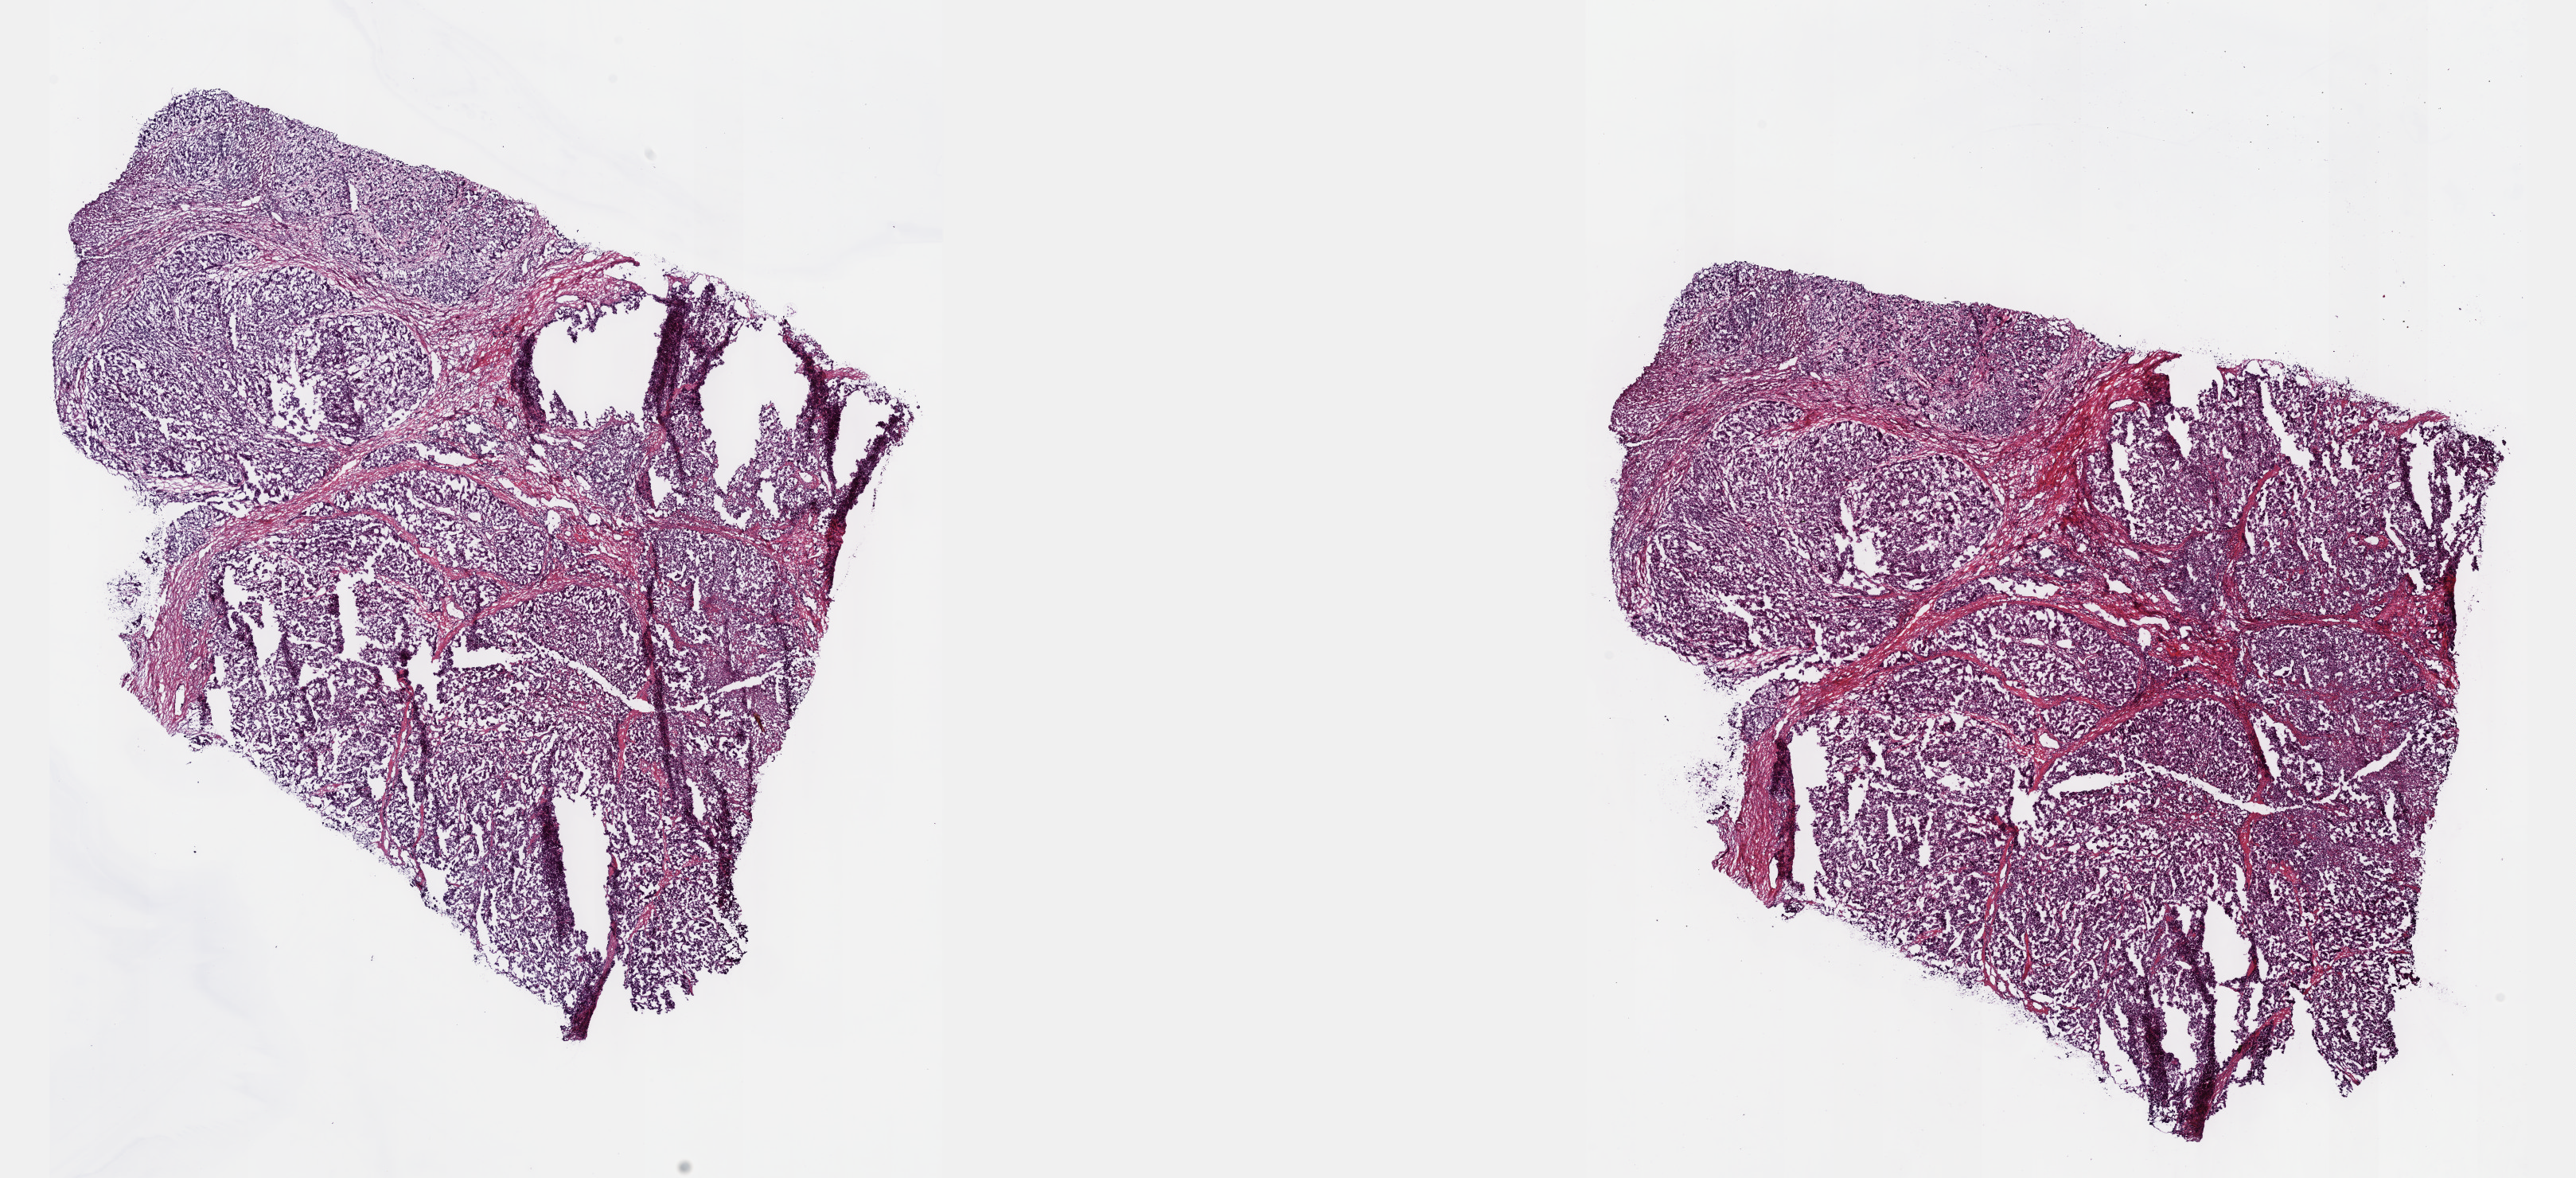
Digitized Hematoxylin and eosin (H&E) stained tissue section (whole slide), a low-resolution overview of the entire scanned area, about 26.2 x 12.0 mm (from a 40x scan), frozen section from the top of the tissue portion, primary tumour sample from the liver. Patient: female, age at initial diagnosis 64 years. Histologic grade: G3 (poorly differentiated). Slide review estimates, as recorded: tumour cells 90%, tumour nuclei 95%, normal cells 0%, stromal cells 10%, necrosis 0%. Infiltration values recorded for this section: lymphocyte infiltration 0%, monocyte infiltration 0%, neutrophil infiltration 0%.
• pathologic diagnosis: Hepatocellular carcinoma, NOS
• AJCC pathologic stage: I (7th edition)